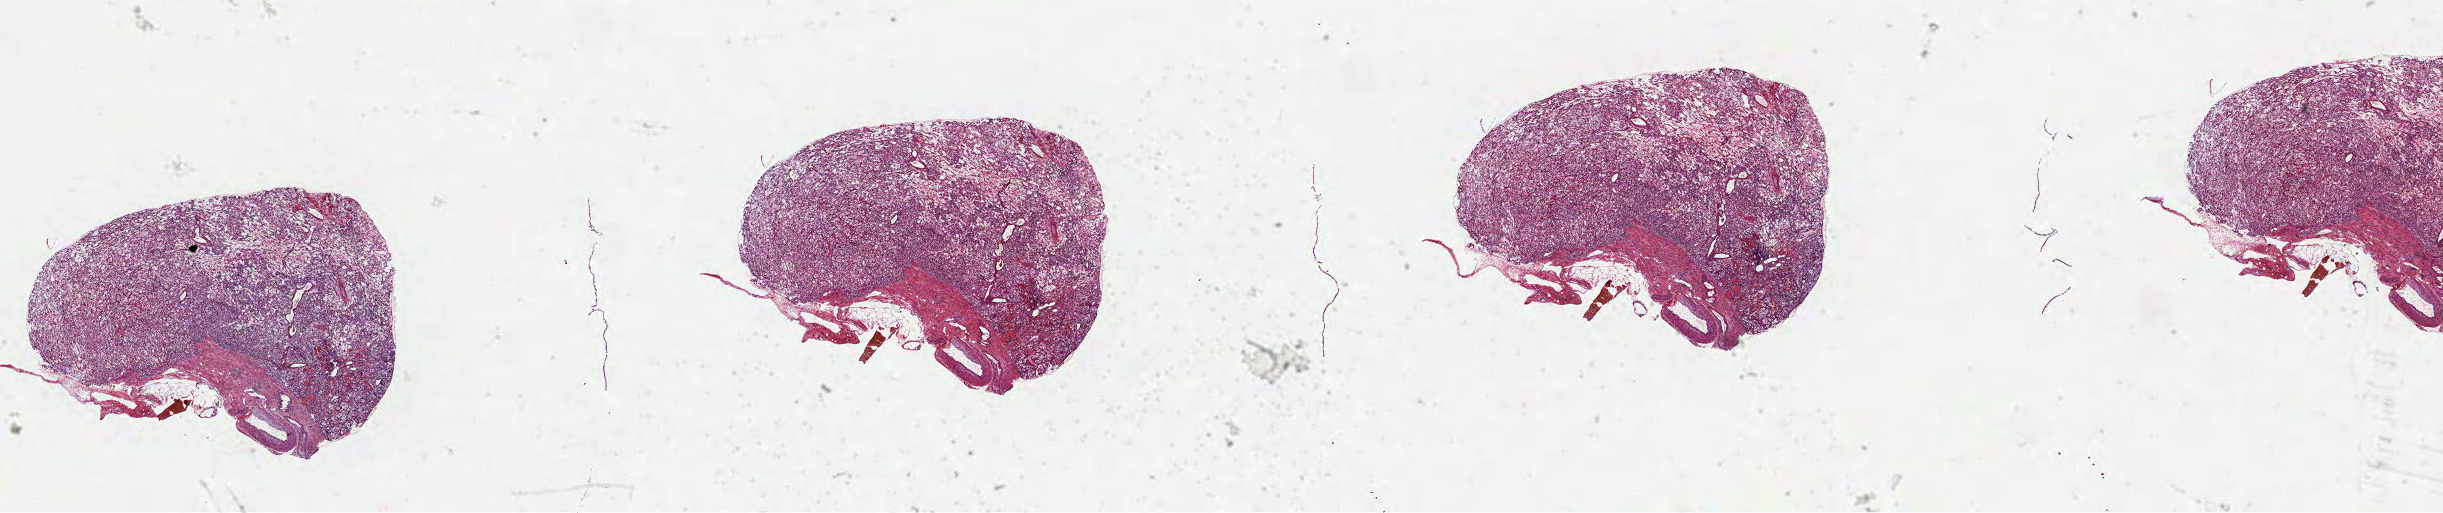
H&E whole-slide image — low-resolution overview of the scanned area, about 39.4 x 8.3 mm (from a 40x scan). Formalin-fixed paraffin-embedded (FFPE) diagnostic section. Primary tumour sample from the kidney. Male patient; age at initial diagnosis 79 years. Histologic grade: G2 (moderately differentiated).
Pathologic diagnosis: Clear cell adenocarcinoma, NOS. Laterality: right. AJCC pathologic stage: I. TNM: T1a NX M0.